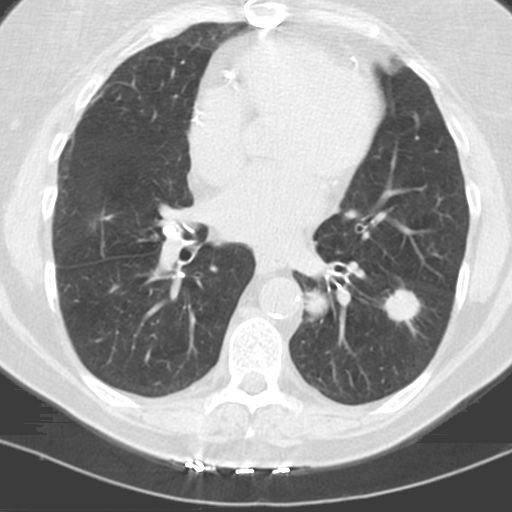
Low-dose screening chest CT, one axial slice; slice 51 of 121 in the series (ordered by position); lung window (W 1500 / L -600 HU); 3.2 mm slice thickness; 512 × 512 image matrix, field of view 278 × 278 mm.
Annotated regions visible in this slice (manually delineated by an expert):
- lesion 1 (tumor, lower lobe of left lung): bounding box (x1, y1, x2, y2) in pixels: (385, 289, 421, 322)
- lesion 2 (tumor, lower lobe of left lung): (305, 290, 328, 314)